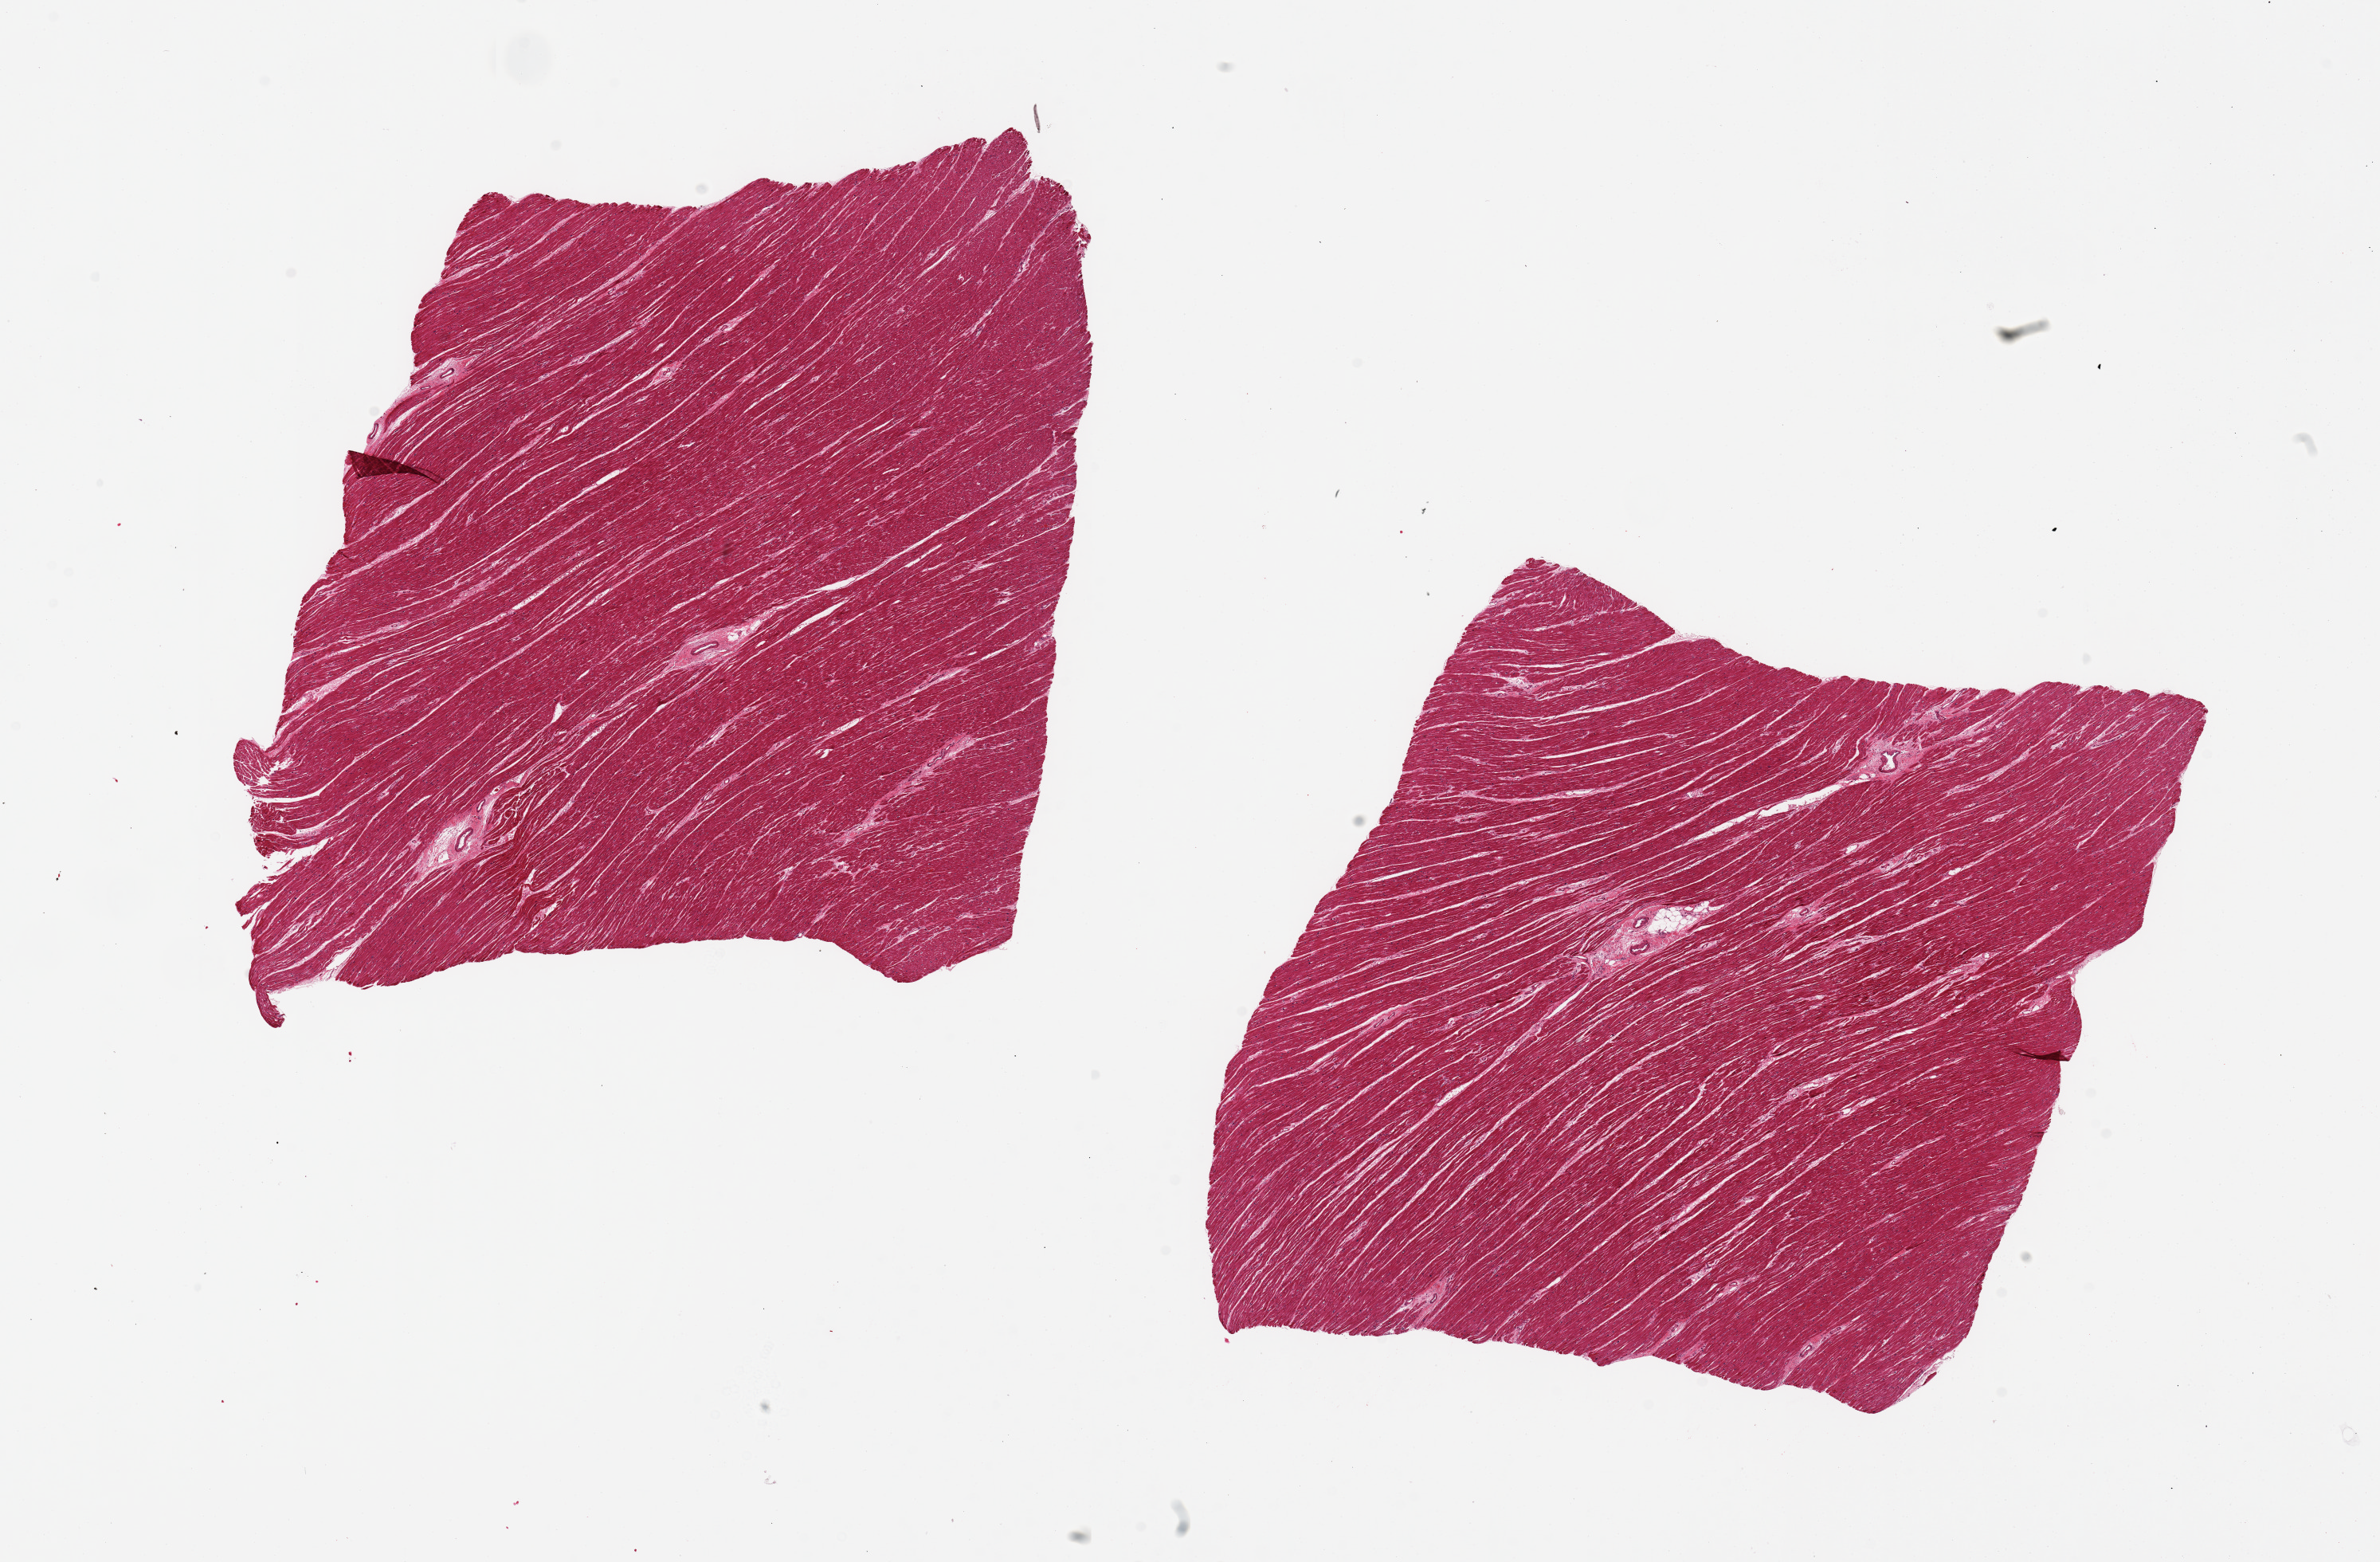
Whole-slide image, H&E stain — whole scanned area (about 23.6 x 15.5 mm) shown as a low-resolution overview, PAXgene-fixed, paraffin-embedded tissue, sampled site (target tissue): heart, tissue donor sample. Donor: male.
Reviewer comment on this tissue sample: 2 pieces, 7.5x7.5 and 7x7mm; mild interstitial fibrosis.